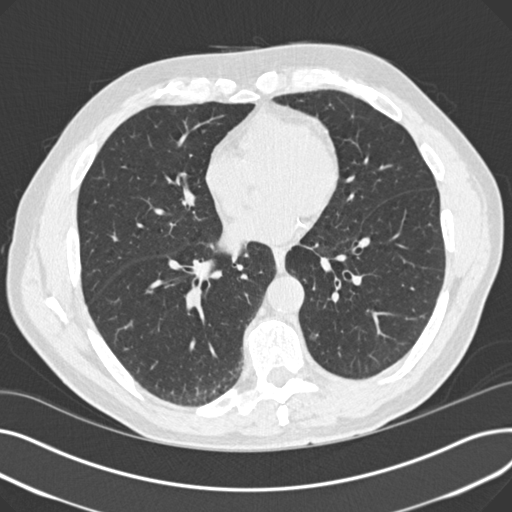
Axial slice from a low-dose chest CT screening exam; second screening round (one year after baseline); lung window (W 1500 / L -600 HU); 2 mm slice thickness; standard (soft-tissue) reconstruction kernel (B30f). Male participant, aged 64 years at enrolment. Former smoker at enrolment.
Expert-annotated lung lesion, bounding box (x1, y1, x2, y2) in pixels: (297, 317, 334, 350). Screening reader's record for this exam (one nodule recorded; not confirmed to be the boxed lesion): non-calcified nodule or mass ≥4 mm, left lower lobe, 6 × 5 mm, smooth margins, ground glass attenuation, pre-existing on the prior screen: yes; interval growth: no. Official screen result: positive, no significant change: stable abnormalities potentially related to lung cancer, unchanged since the prior screening exam. Lung cancer was diagnosed 417 days after this screen (after the third annual screen): adenocarcinoma with mixed subtypes, left lower lobe, well differentiated (G1), stage IA (AJCC 6th edition), 7 mm at pathology.